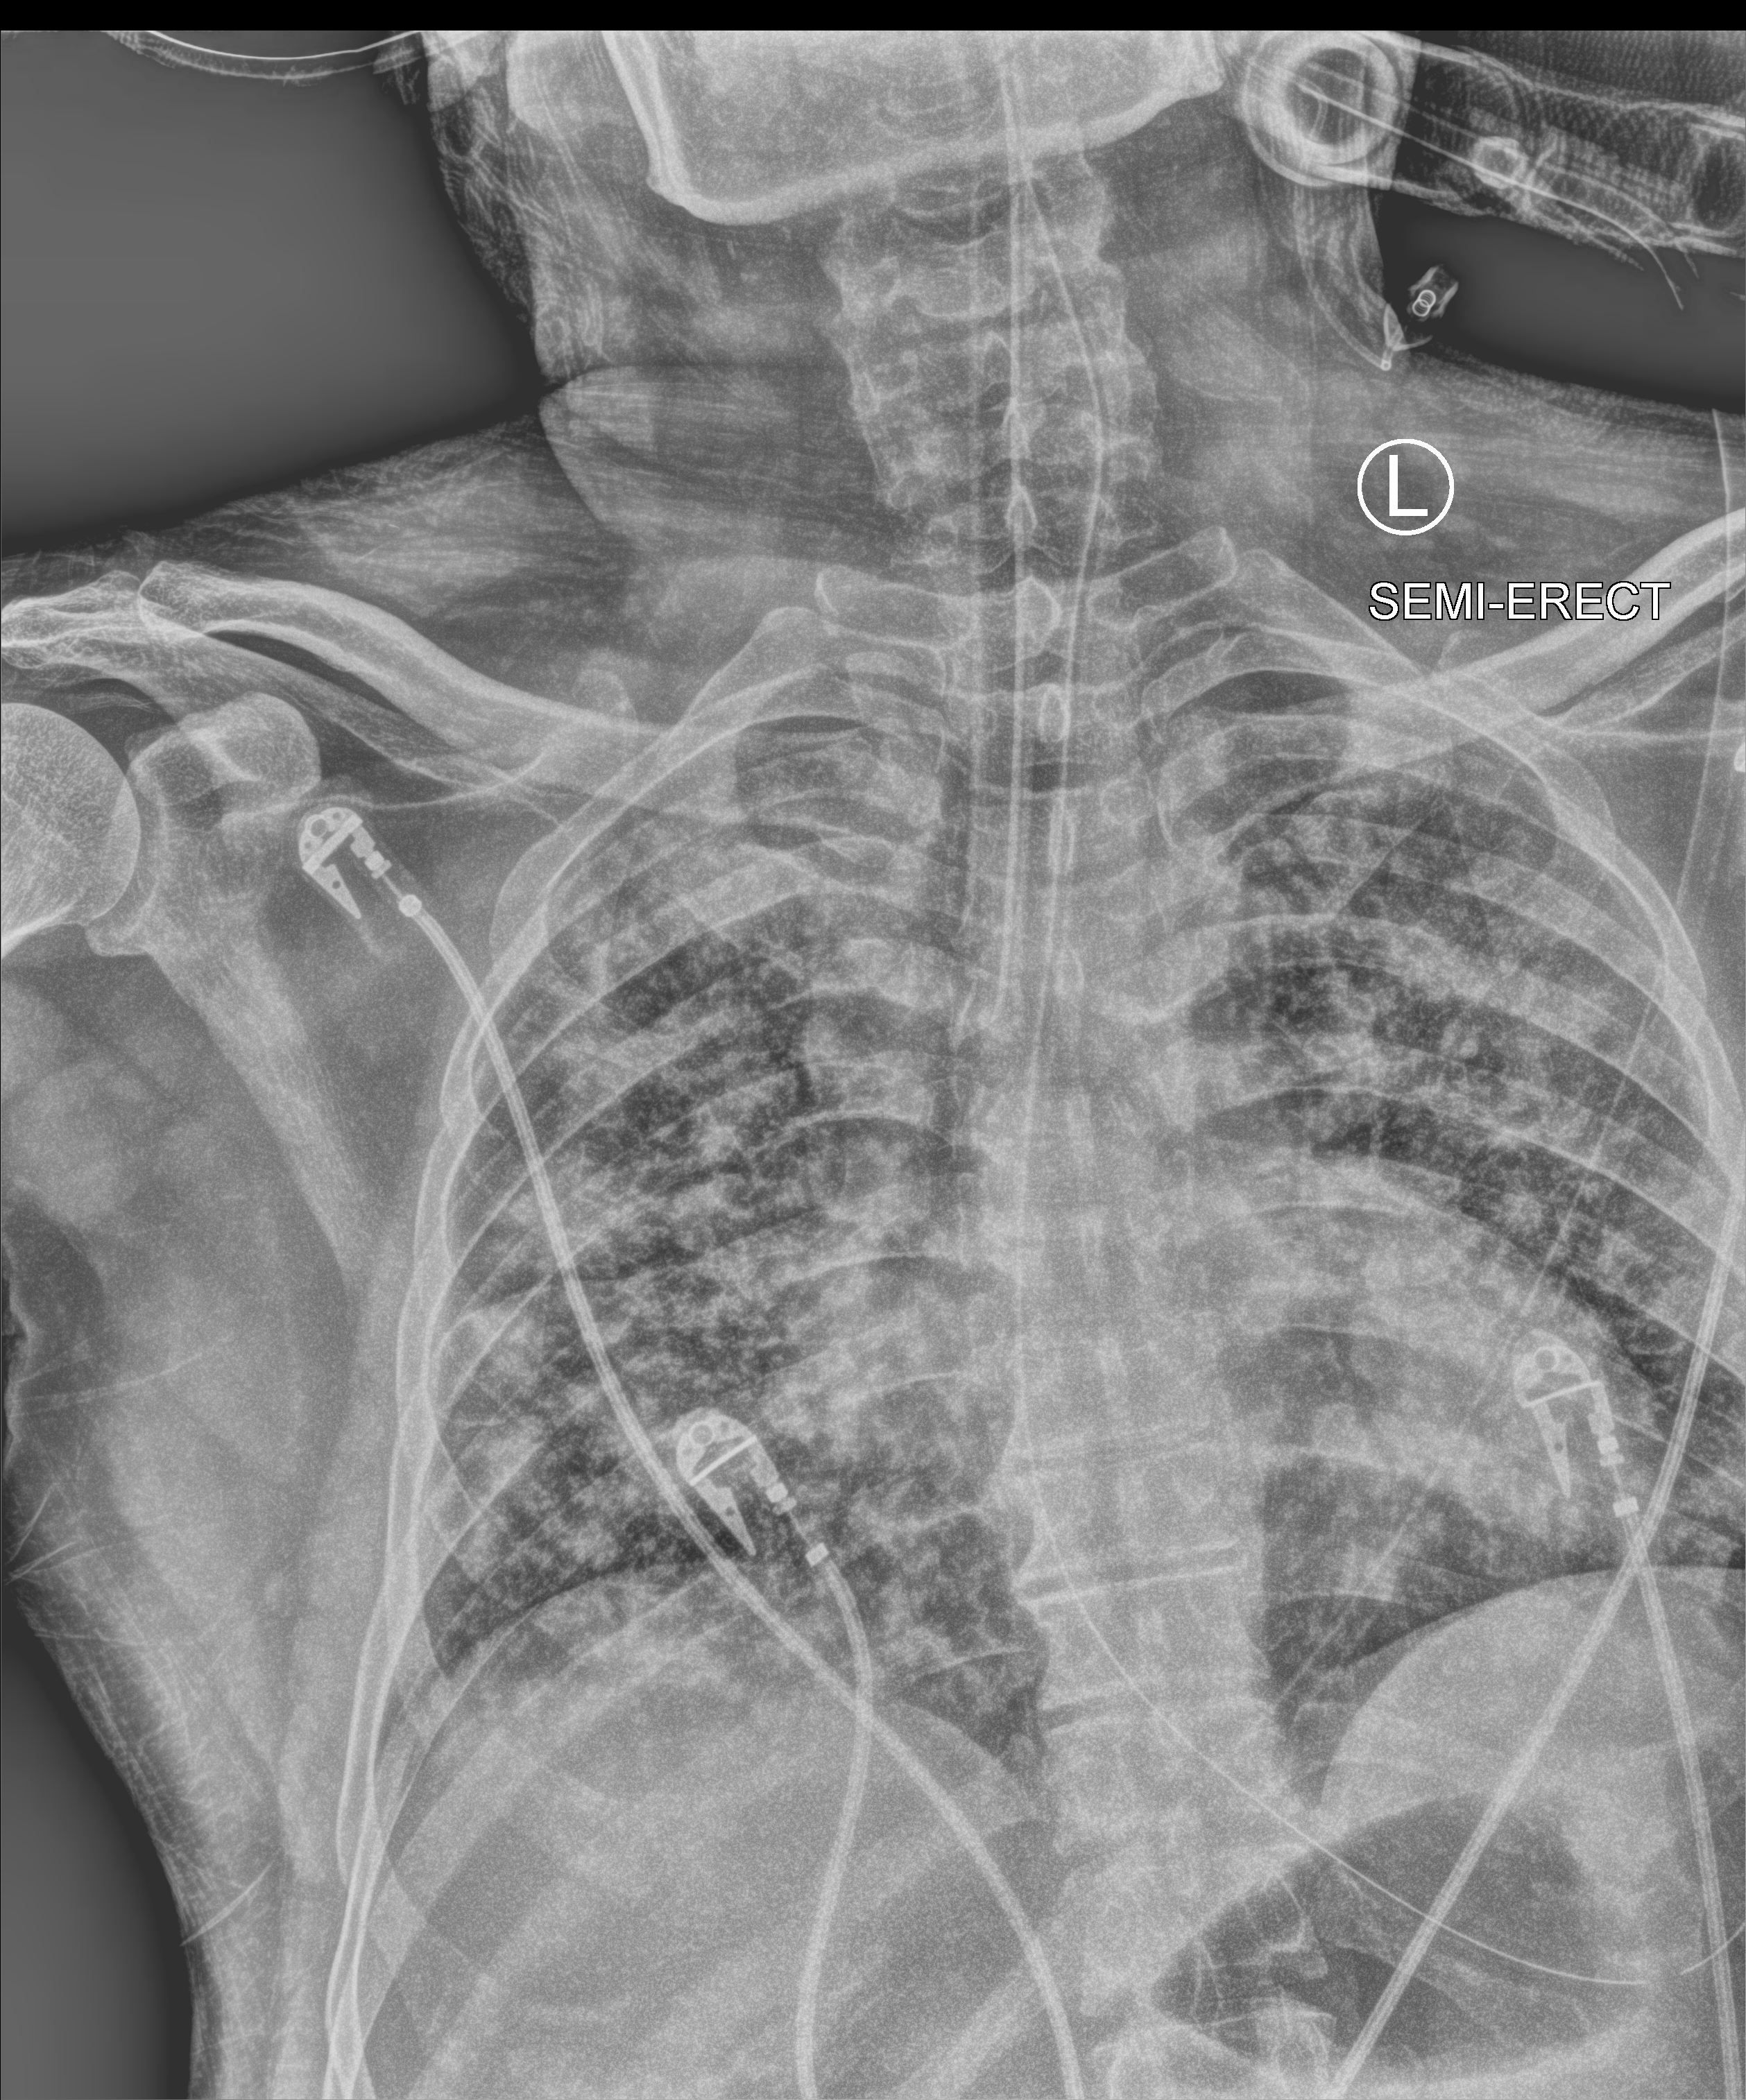
Bedside chest radiograph (computed radiography); anteroposterior (AP) projection. Male patient hospitalised with COVID-19, age 18–59 years.
From the hospital-stay record, not from the radiograph (when in the stay this image was taken is not recorded):
- admitted to intensive care during this hospital stay: yes
- mechanically ventilated during this hospital stay: yes